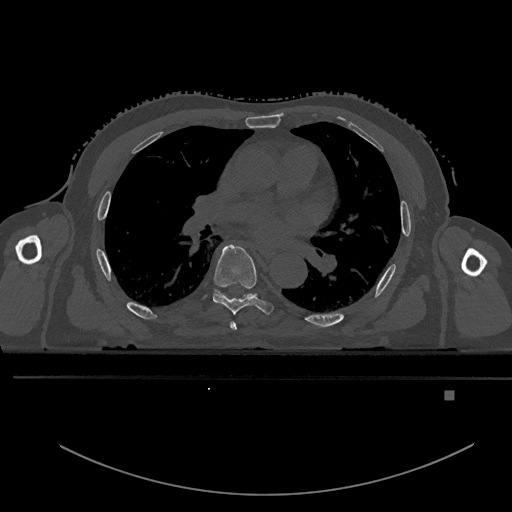
CT including the spine, one axial slice; position 304 of 969 along the scan axis; bone window (W 1800 / L 400 HU); 0.5 mm slice thickness; 512 × 512 image matrix. Patient: male, 82 years. From the clinical record (not read from this slice): primary cancer: prostate; vertebrae with lytic lesions (as recorded): T11, T9, T8, T2.
Outlined on this slice (semi-automatically segmented with operator editing):
- T5 vertebra: bounding box <230,321,237,331> (left, top, right, bottom; pixels)
- T6 vertebra: <212,244,274,315>
- T7 vertebra: <249,295,251,297>